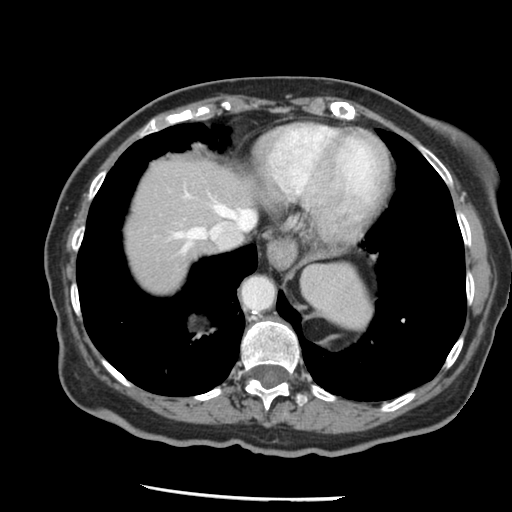
Contrast-enhanced abdominal CT, one axial slice. Position 116 of 148 along the scan axis. Reconstruction kernel STANDARD. 120 kVp. Intravenous contrast given. Soft-tissue window (W 400 / L 40 HU). 512 × 512 image matrix, field of view 330 × 330 mm. Female patient, age 85 years. Case-level facts recorded for this patient, not image findings: diagnosis: colorectal cancer liver metastases, imaged before liver resection; multiple liver metastases: no; largest metastasis: 0.9 cm.
Annotated regions visible in this slice (outlined manually by an expert reader):
- hepatic veins: box from (x=174, y=204) to (x=255, y=253) px
- liver: (x=123, y=156)–(x=258, y=297)
- planned liver remnant (the part of the liver to remain after resection): (x=123, y=156)–(x=258, y=297)